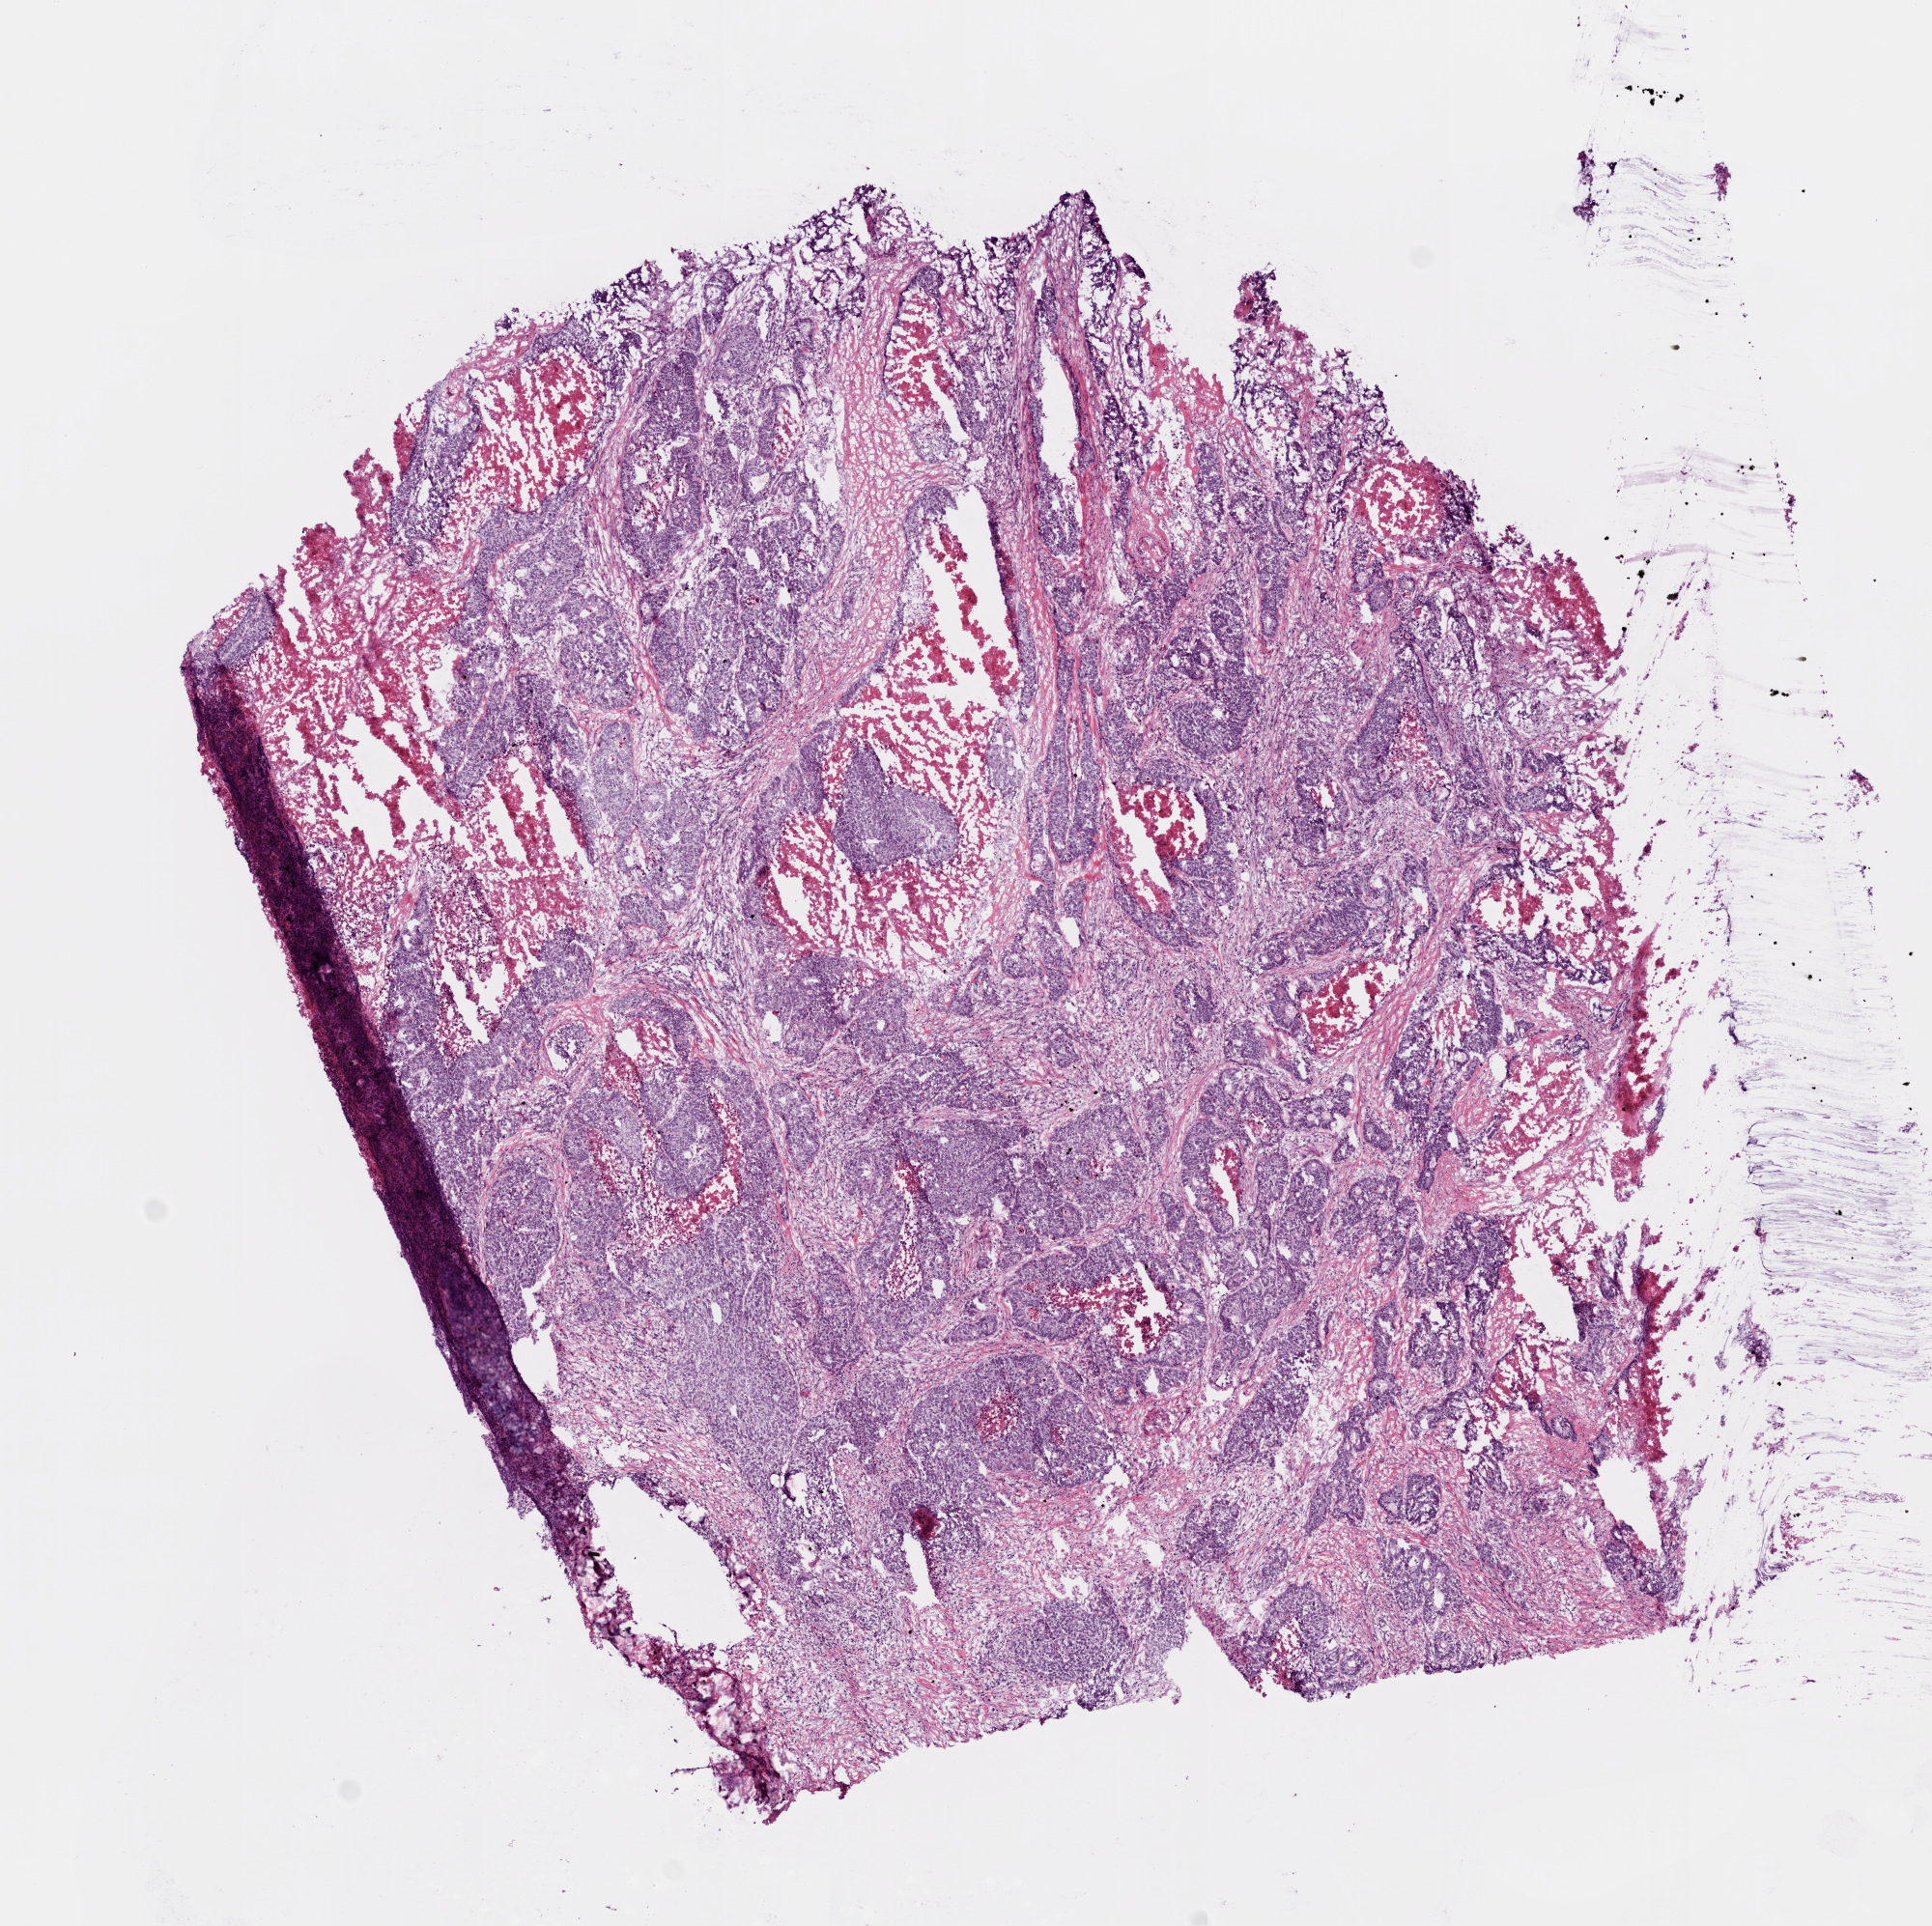
Digitized Hematoxylin and eosin (H&E) stained tissue section (whole slide) — shown as a low-resolution overview of the whole scanned area (about 8.0 x 8.0 mm); frozen section; primary tumour sample from the stomach. Patient: male, age at initial diagnosis 66 years.
Histologic diagnosis: Adenocarcinoma, intestinal type (body of stomach).